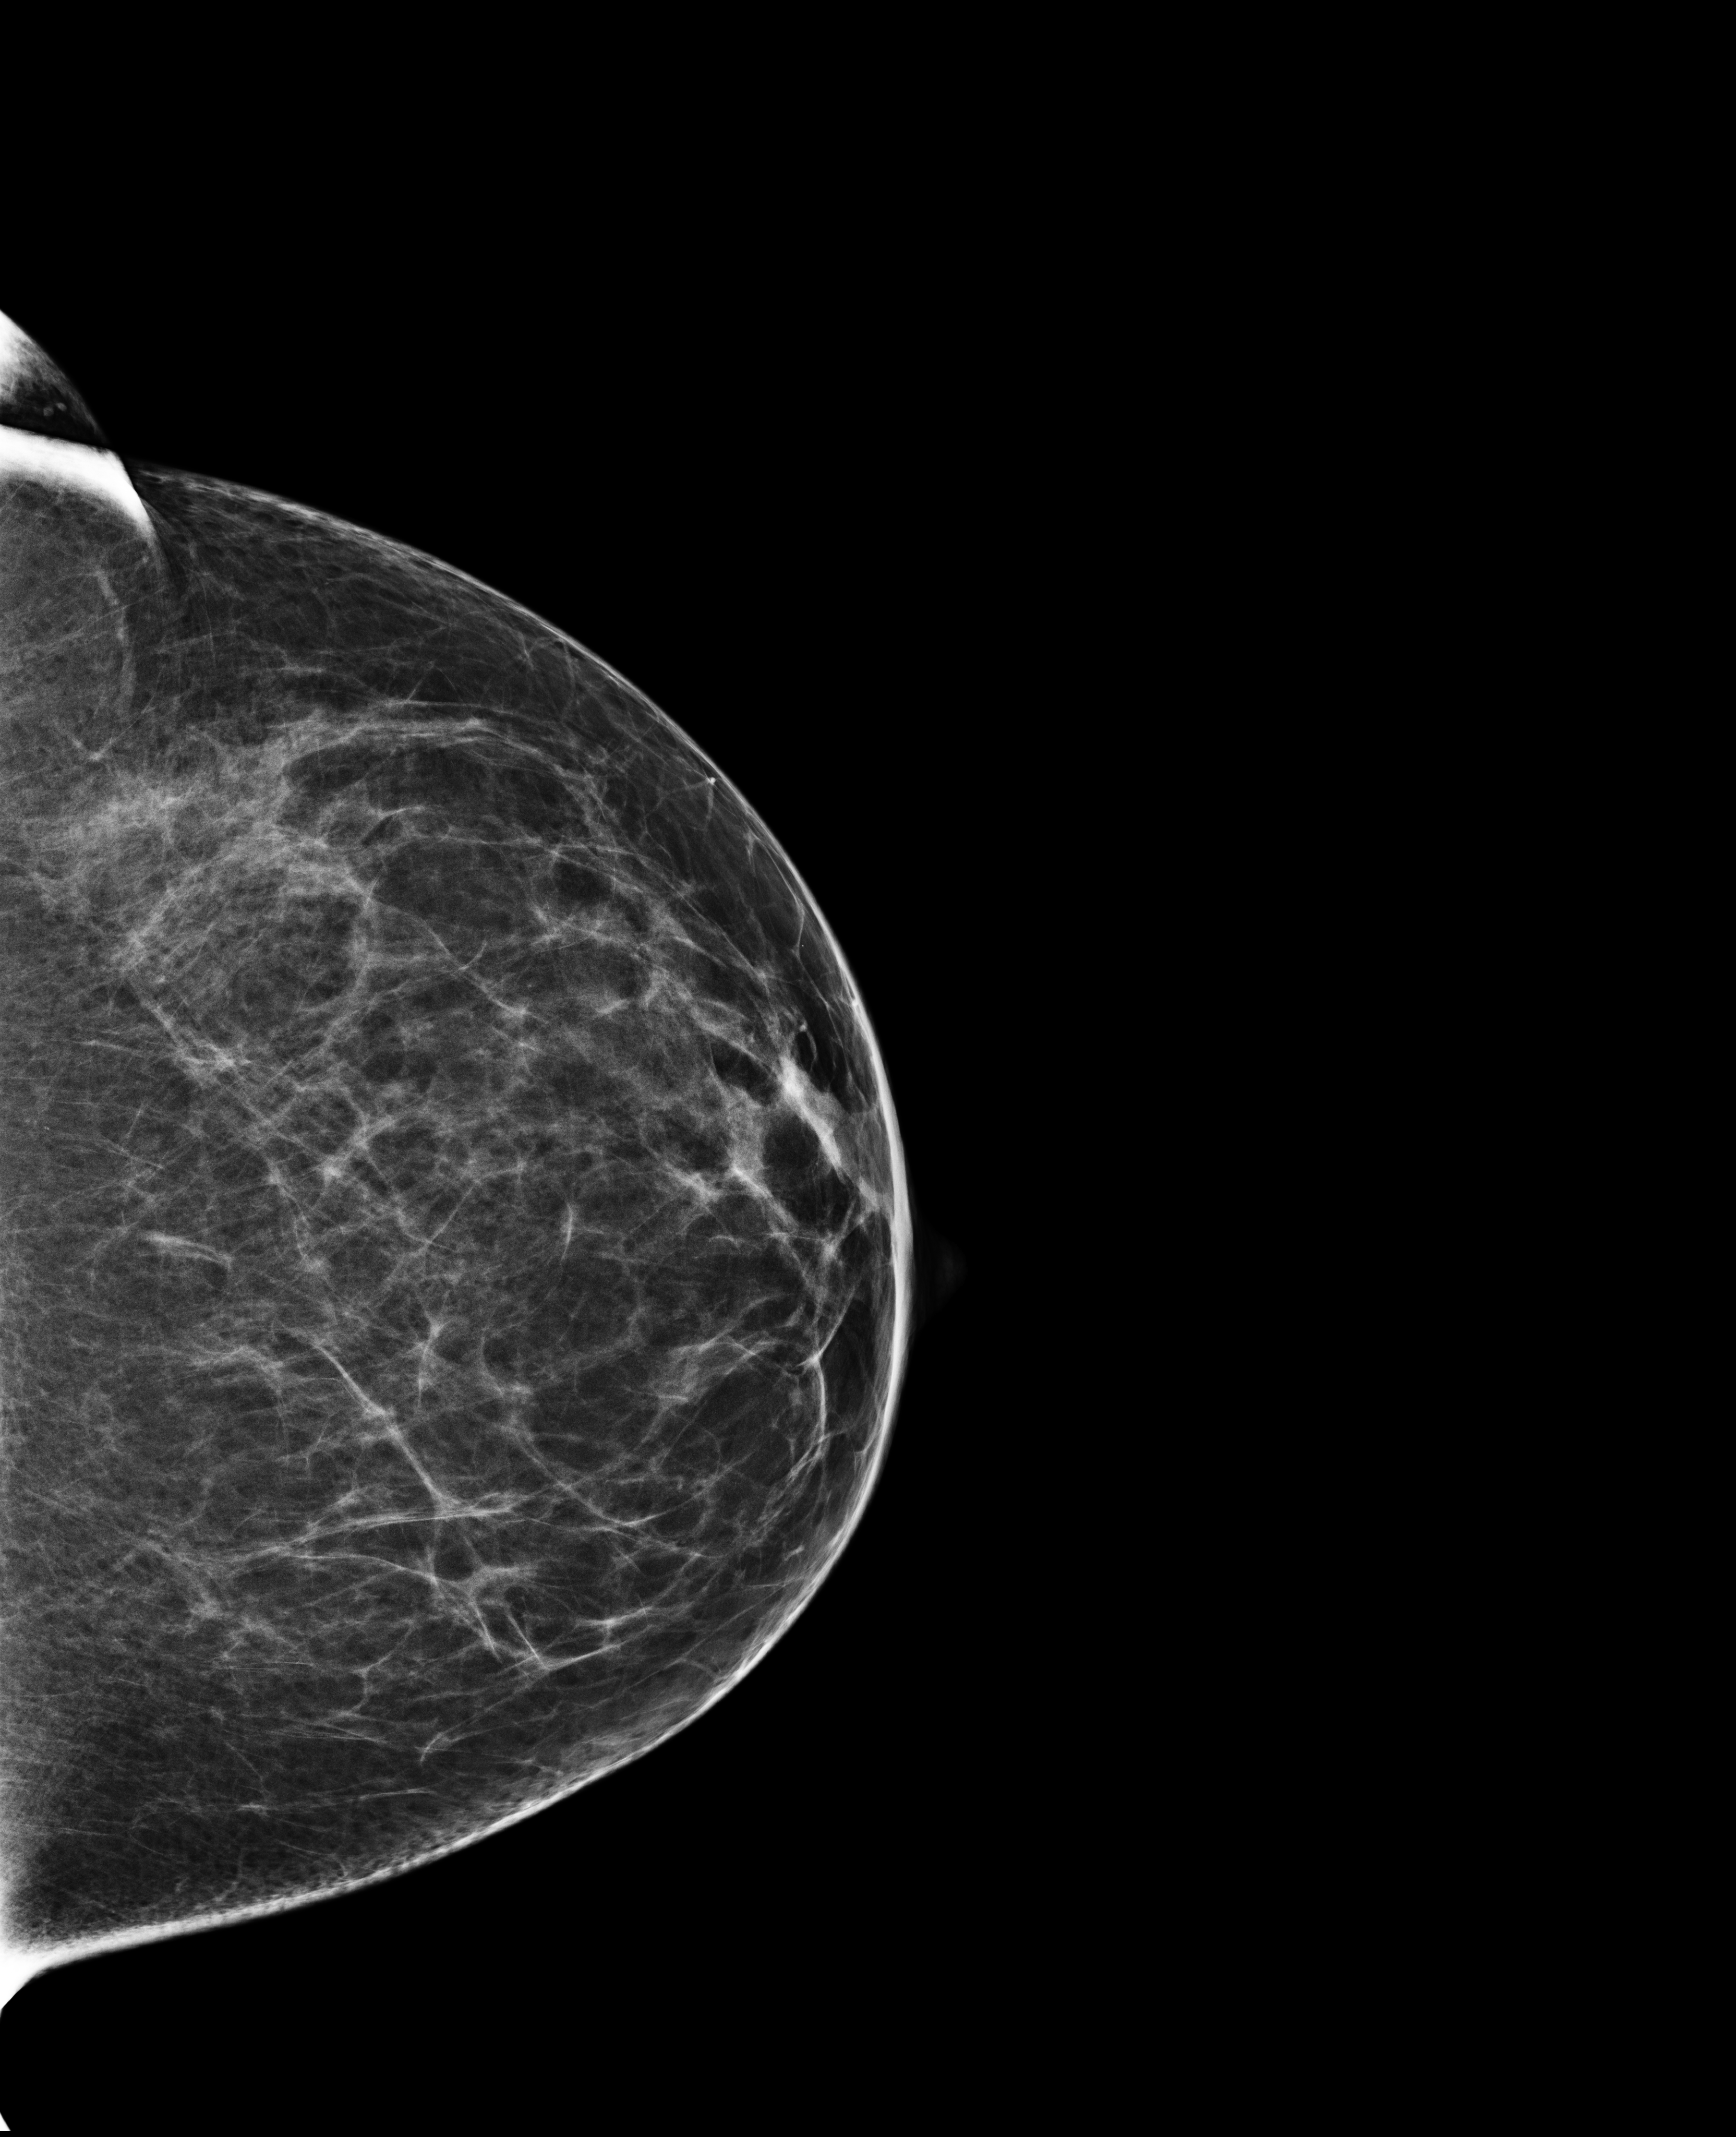
Digital mammogram (FFDM); left breast; CC view; annual screening mammography examination; system: Selenia Dimensions. Female patient, age 41 years.
Breast density at the screening exam (both breasts): heterogeneously dense (BI-RADS density category c). Final BI-RADS category for the screening round (tomosynthesis exam, both breasts): category 1. Recall: no recall after this screen.